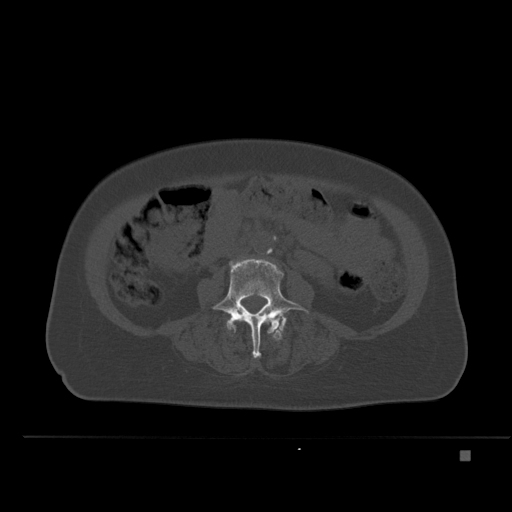
CT including the spine, one axial slice. Position 180 of 477 along the scan axis. Bone window (W 1800 / L 400 HU). 512 × 512 image matrix, field of view 422 × 422 mm. Patient: female, 74 years. From the clinical record (not read from this slice): primary cancer: colon.
Outlined on this slice (semi-automatic segmentation, software-assisted and operator-edited):
- L4 vertebra: bounding box [x1, y1, x2, y2] px = [212, 259, 309, 358]
- L5 vertebra: [273, 321, 286, 340]